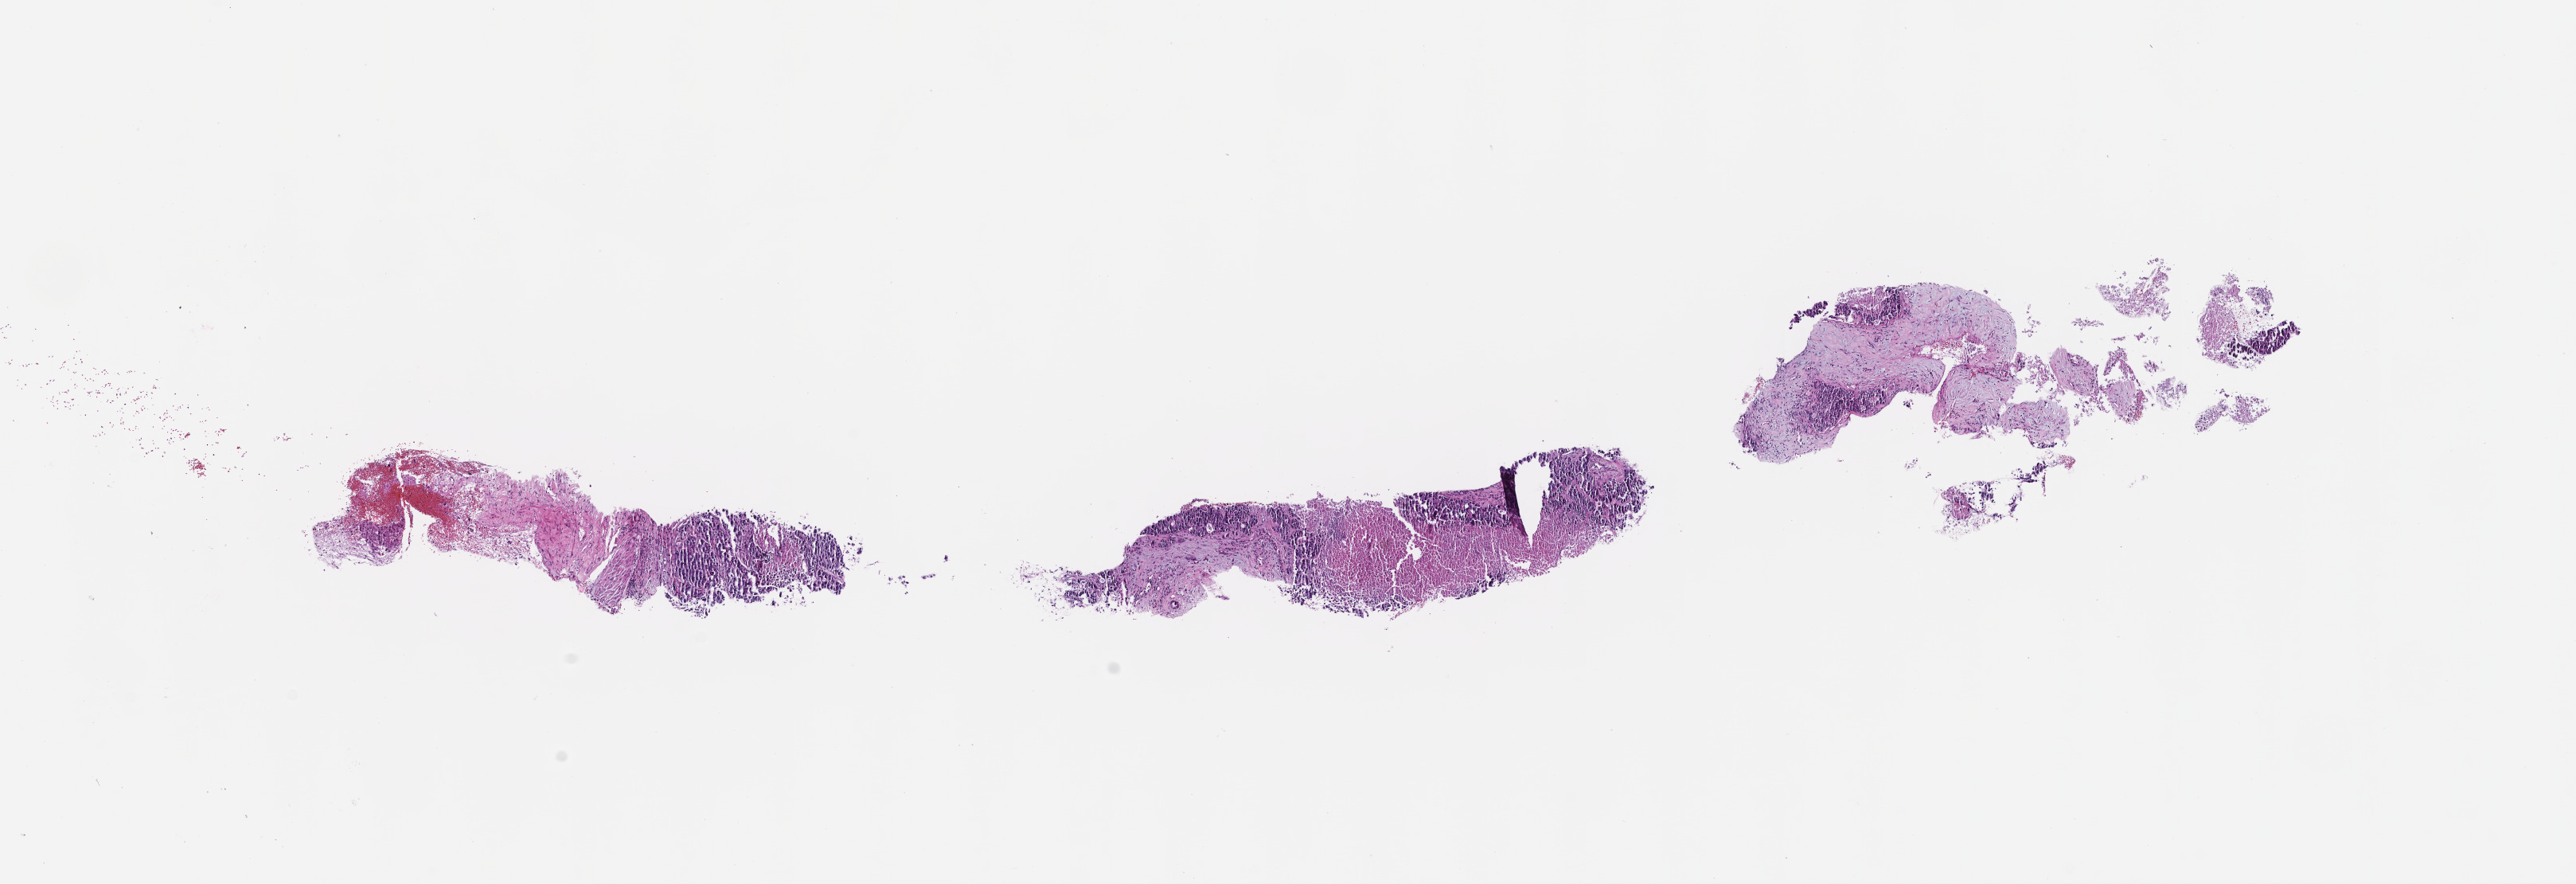
H&E whole-slide image, shown as a low-resolution overview of the whole scanned area (about 13.1 x 4.5 mm), formalin-fixed paraffin-embedded section. Patient: female.
This section: metastatic tumor tissue. Patient diagnosis (primary): Colorectal Carcinoma.